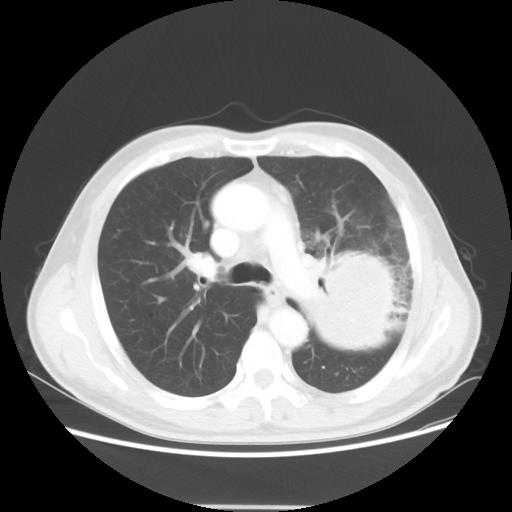
Chest CT, one axial slice; slice 34 of 53 in the series (ordered by position); reconstruction kernel STANDARD; lung window (W 1500 / L -600 HU); 5 mm slice thickness; 512 × 512 image matrix. Patient: male, 60 years. From the clinical record (not read from this slice): clinical TNM (as recorded): T4 N1 M1a.
Outlined on this slice (bounding box drawn by a radiologist):
- lung tumour (recorded histology: large cell carcinoma): bounding box <305,245,407,353> (left, top, right, bottom; pixels)